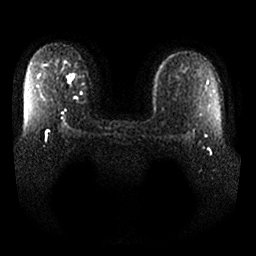
Breast MRI, one axial slice. Slice 25 of 25 in the series (ordered by position). Diffusion-weighted series; image 2 of 4 stored at this slice position (different b-values; order by instance number). 1.5 T. 256 × 256 image matrix. Female patient.
Outlined on this slice (expert manual segmentation):
- tumour on diffusion-weighted imaging: box from (x=66, y=70) to (x=76, y=88) px